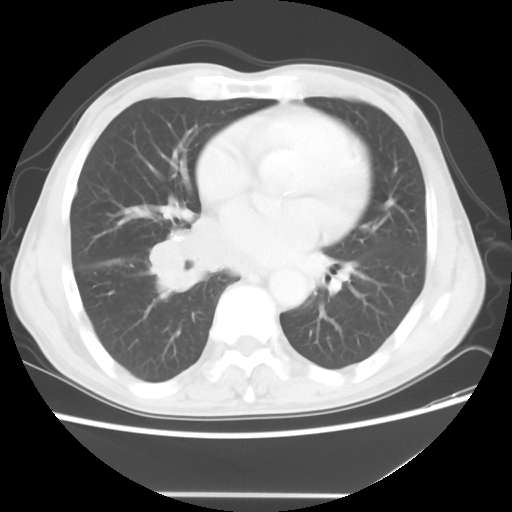
Chest CT, one axial slice; position 24 of 56 along the scan axis; 120 kVp; lung window (W 1500 / L -600 HU); 5 mm slice thickness; 512 × 512 image matrix. Male patient, age 65 years. From the clinical record (not read from this slice): clinical TNM (as recorded): T1c N3 M0; histopathological grade: G3.
Structures marked on this image (bounding box drawn by a radiologist):
- lung tumour (recorded histology: small cell carcinoma): bounding box [x1, y1, x2, y2] px = [141, 212, 266, 293]